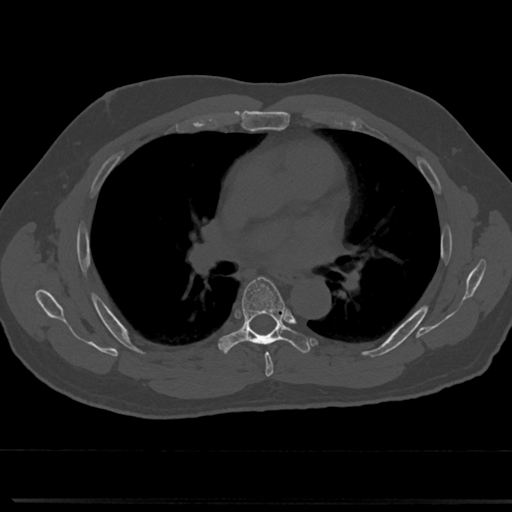
CT including the spine, one axial slice; position 461 of 817 along the scan axis; bone window (W 1800 / L 400 HU); 0.5 mm slice thickness; 512 × 512 image matrix. Male patient, age 61 years. From the clinical record (not read from this slice): primary cancer: prostate.
Outlined on this slice (semi-automatic segmentation, software-assisted and operator-edited):
- T5 vertebra: bounding box <256,340,273,368> (left, top, right, bottom; pixels)
- T6 vertebra: <217,275,309,356>